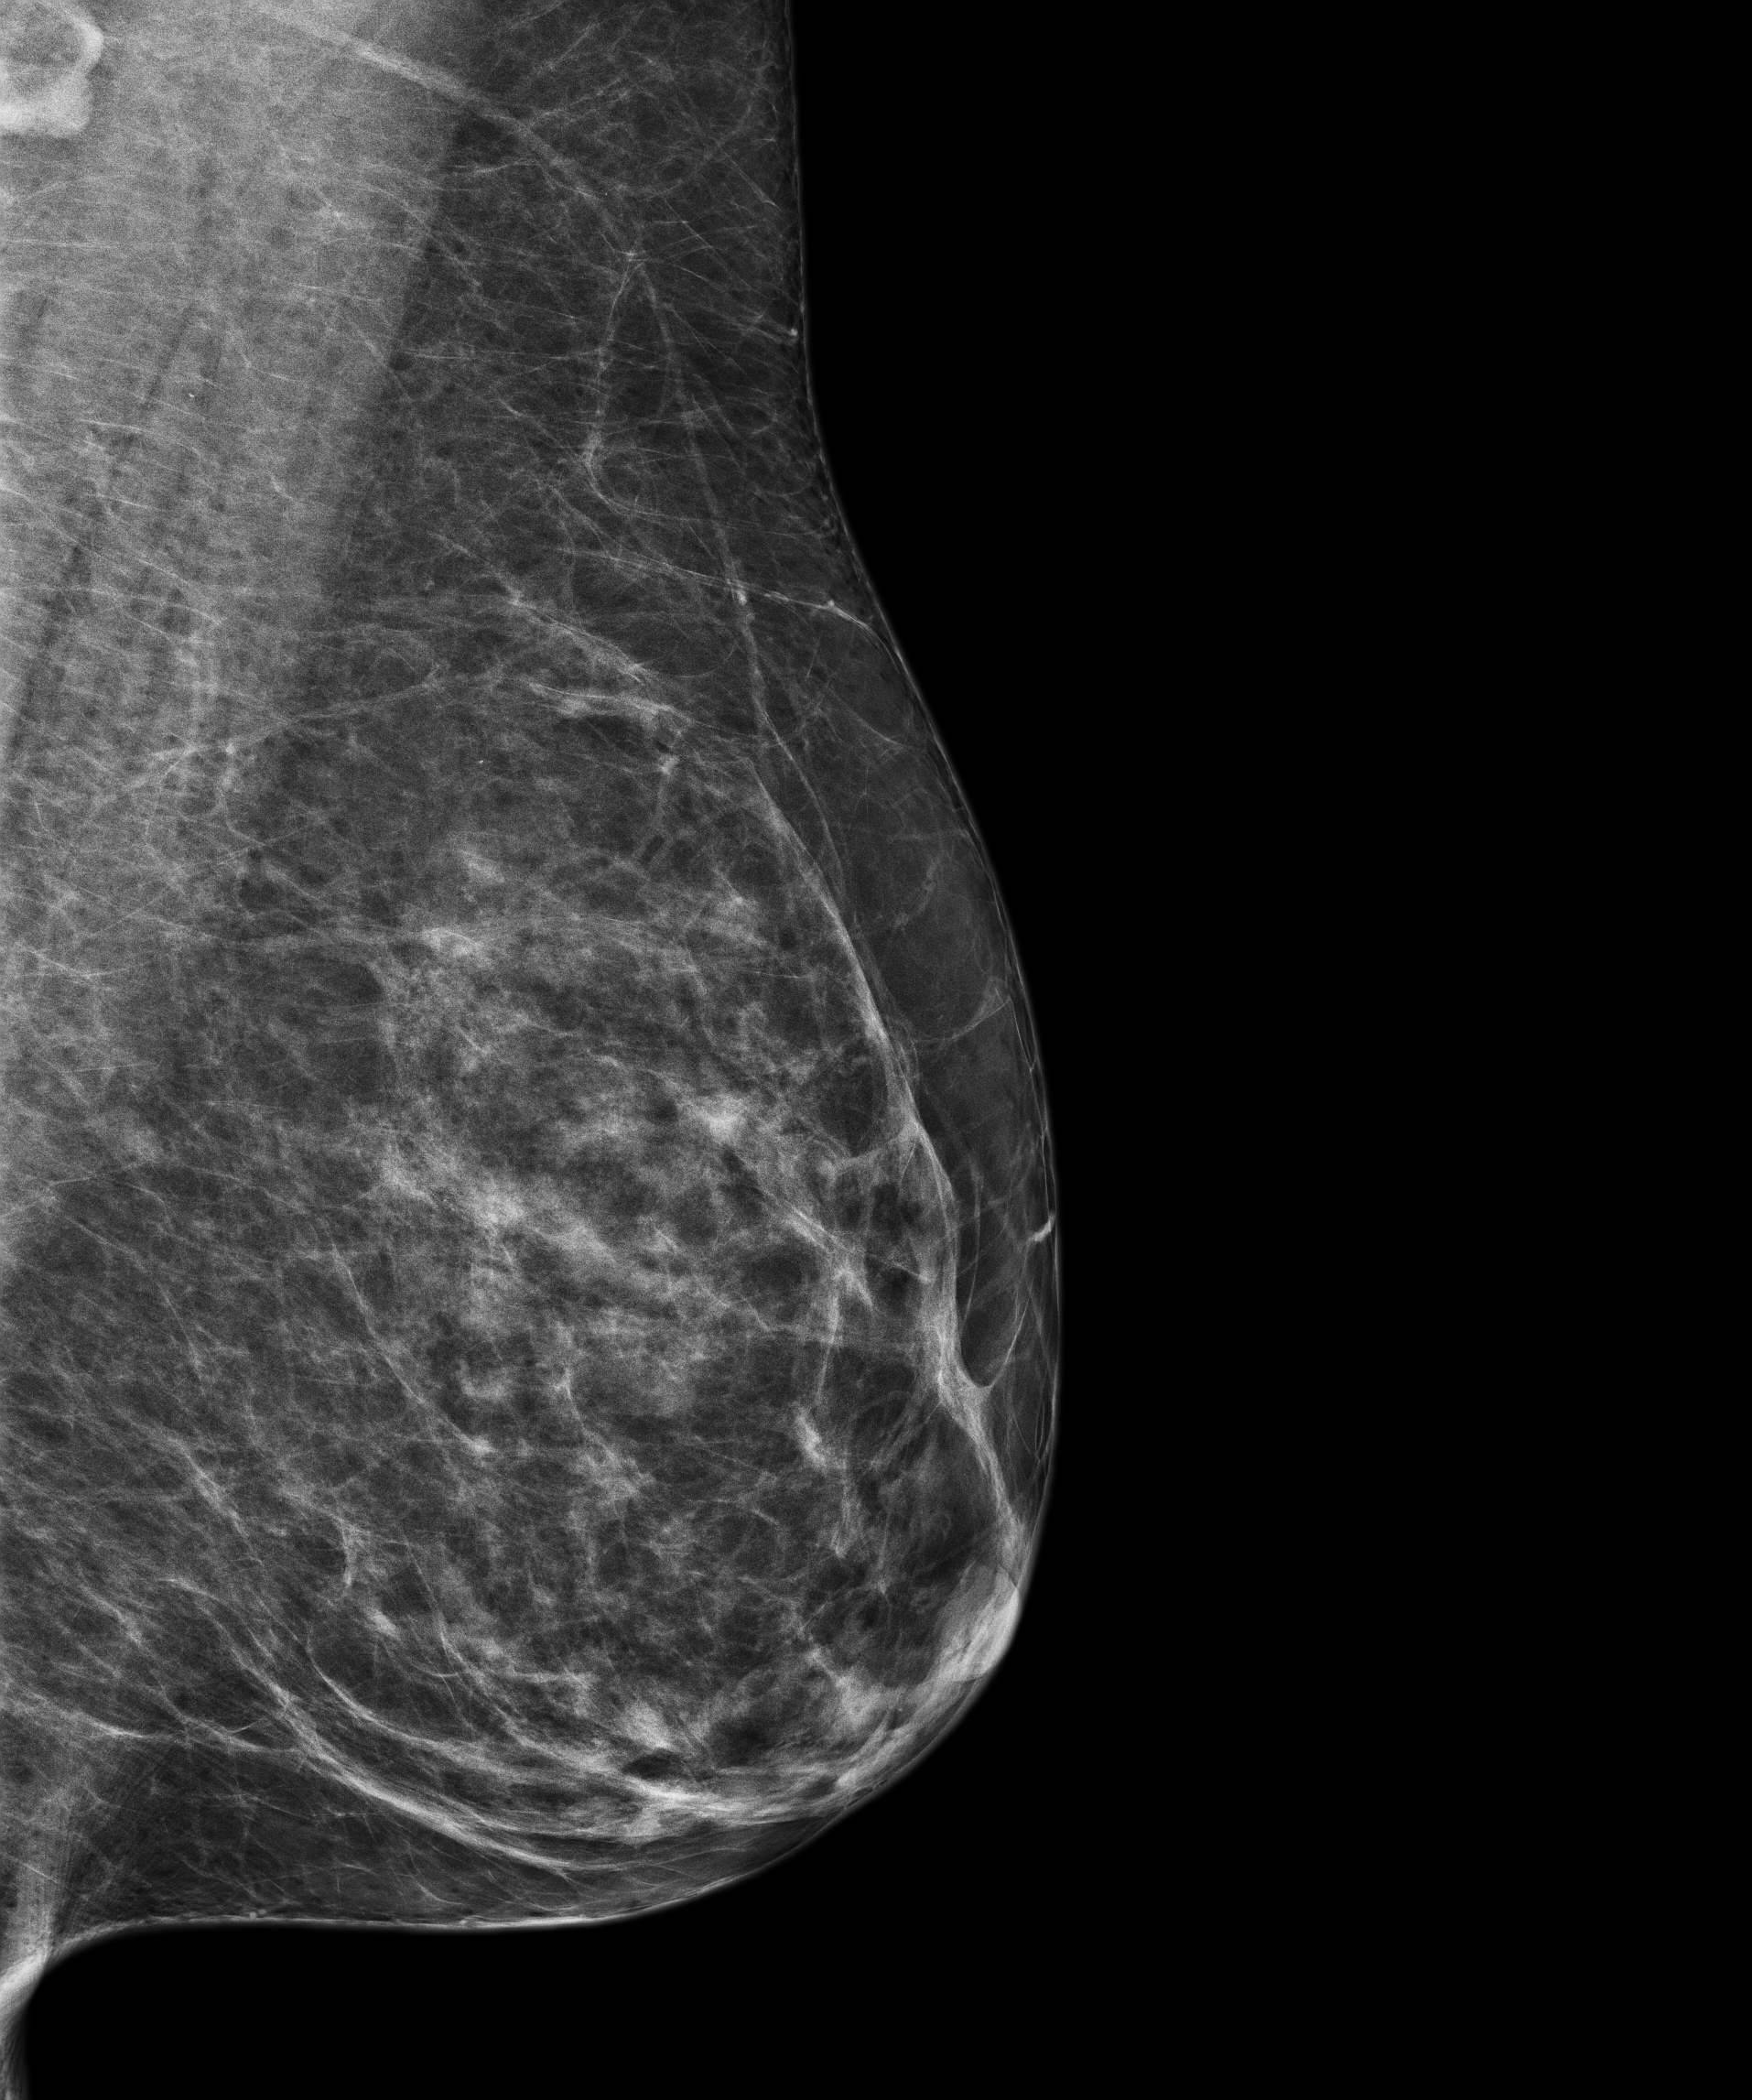
Screening examination. Female patient, age 58 years.
Image type: full-field digital mammogram. Breast: left. Projection: MLO view.